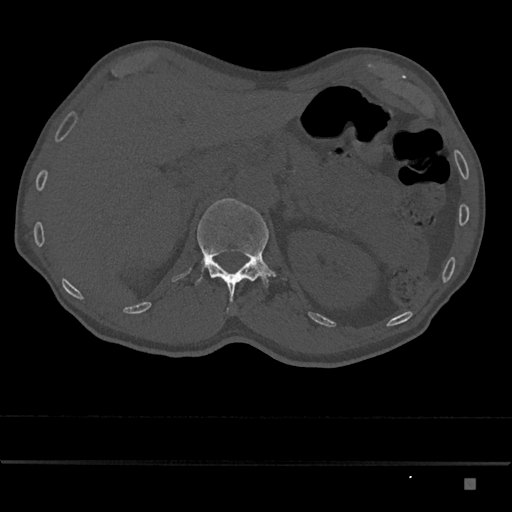
CT including the spine, one axial slice. Position 546 of 797 along the scan axis. Reconstruction kernel Br40s/3. 120 kVp. Bone window (W 1800 / L 400 HU). 0.5 mm slice thickness. 512 × 512 image matrix, field of view 390 × 390 mm. Patient: male, 72 years. Case-level facts recorded for this patient, not image findings: primary cancer: prostate.
Structures marked on this image (semi-automatically segmented with operator editing):
- L1 vertebra: bounding box <195,198,288,312> (left, top, right, bottom; pixels)